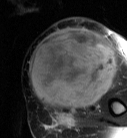
MRI of an extremity soft-tissue mass, one axial slice; position 28 of 87 along the scan axis; T2-weighted fat-saturated; MR volume resampled by the dataset authors to the PET/CT grid (not the native acquisition matrix); 3.27 mm slice thickness; 127 × 138 image matrix, field of view 124 × 135 mm. Female patient. From the clinical record (not read from this slice): histological type: pleiomorphic leiomyosarcoma; grade: high; site of the primary tumour: left biceps.
Outlined on this slice (expert contour drawn on MRI and transferred to this co-registered scan by the dataset authors):
- gross tumour volume including surrounding oedema: bounding box [x1, y1, x2, y2] px = [29, 29, 117, 111]
- gross tumour volume (mass): [29, 29, 117, 108]